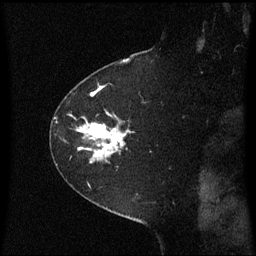
Breast MRI (dynamic contrast-enhanced), one sagittal slice. Slice 48 of 60 in the series (ordered by position). Dynamic contrast-enhanced series, image 2 of 3 at this slice position (ordered by acquisition). 1.5 T. TE 4.2 ms, TR 8.4 ms. 2 mm slice thickness. 256 × 256 image matrix, field of view 210 × 210 mm. Female patient, age 60 years. Case-level facts recorded for this patient, not image findings: setting: breast cancer imaged before/during neoadjuvant chemotherapy; receptor status: triple-negative.
Structures marked on this image (semi-automatically segmented with operator editing):
- analysis volume of interest (the breast-tissue region the enhancement analysis was run in; not a lesion): bounding box [x1, y1, x2, y2] px = [52, 99, 137, 181]
- tumour enhancement mask (voxels above the 70 % enhancement threshold inside the analysis volume of interest): [78, 124, 127, 158]